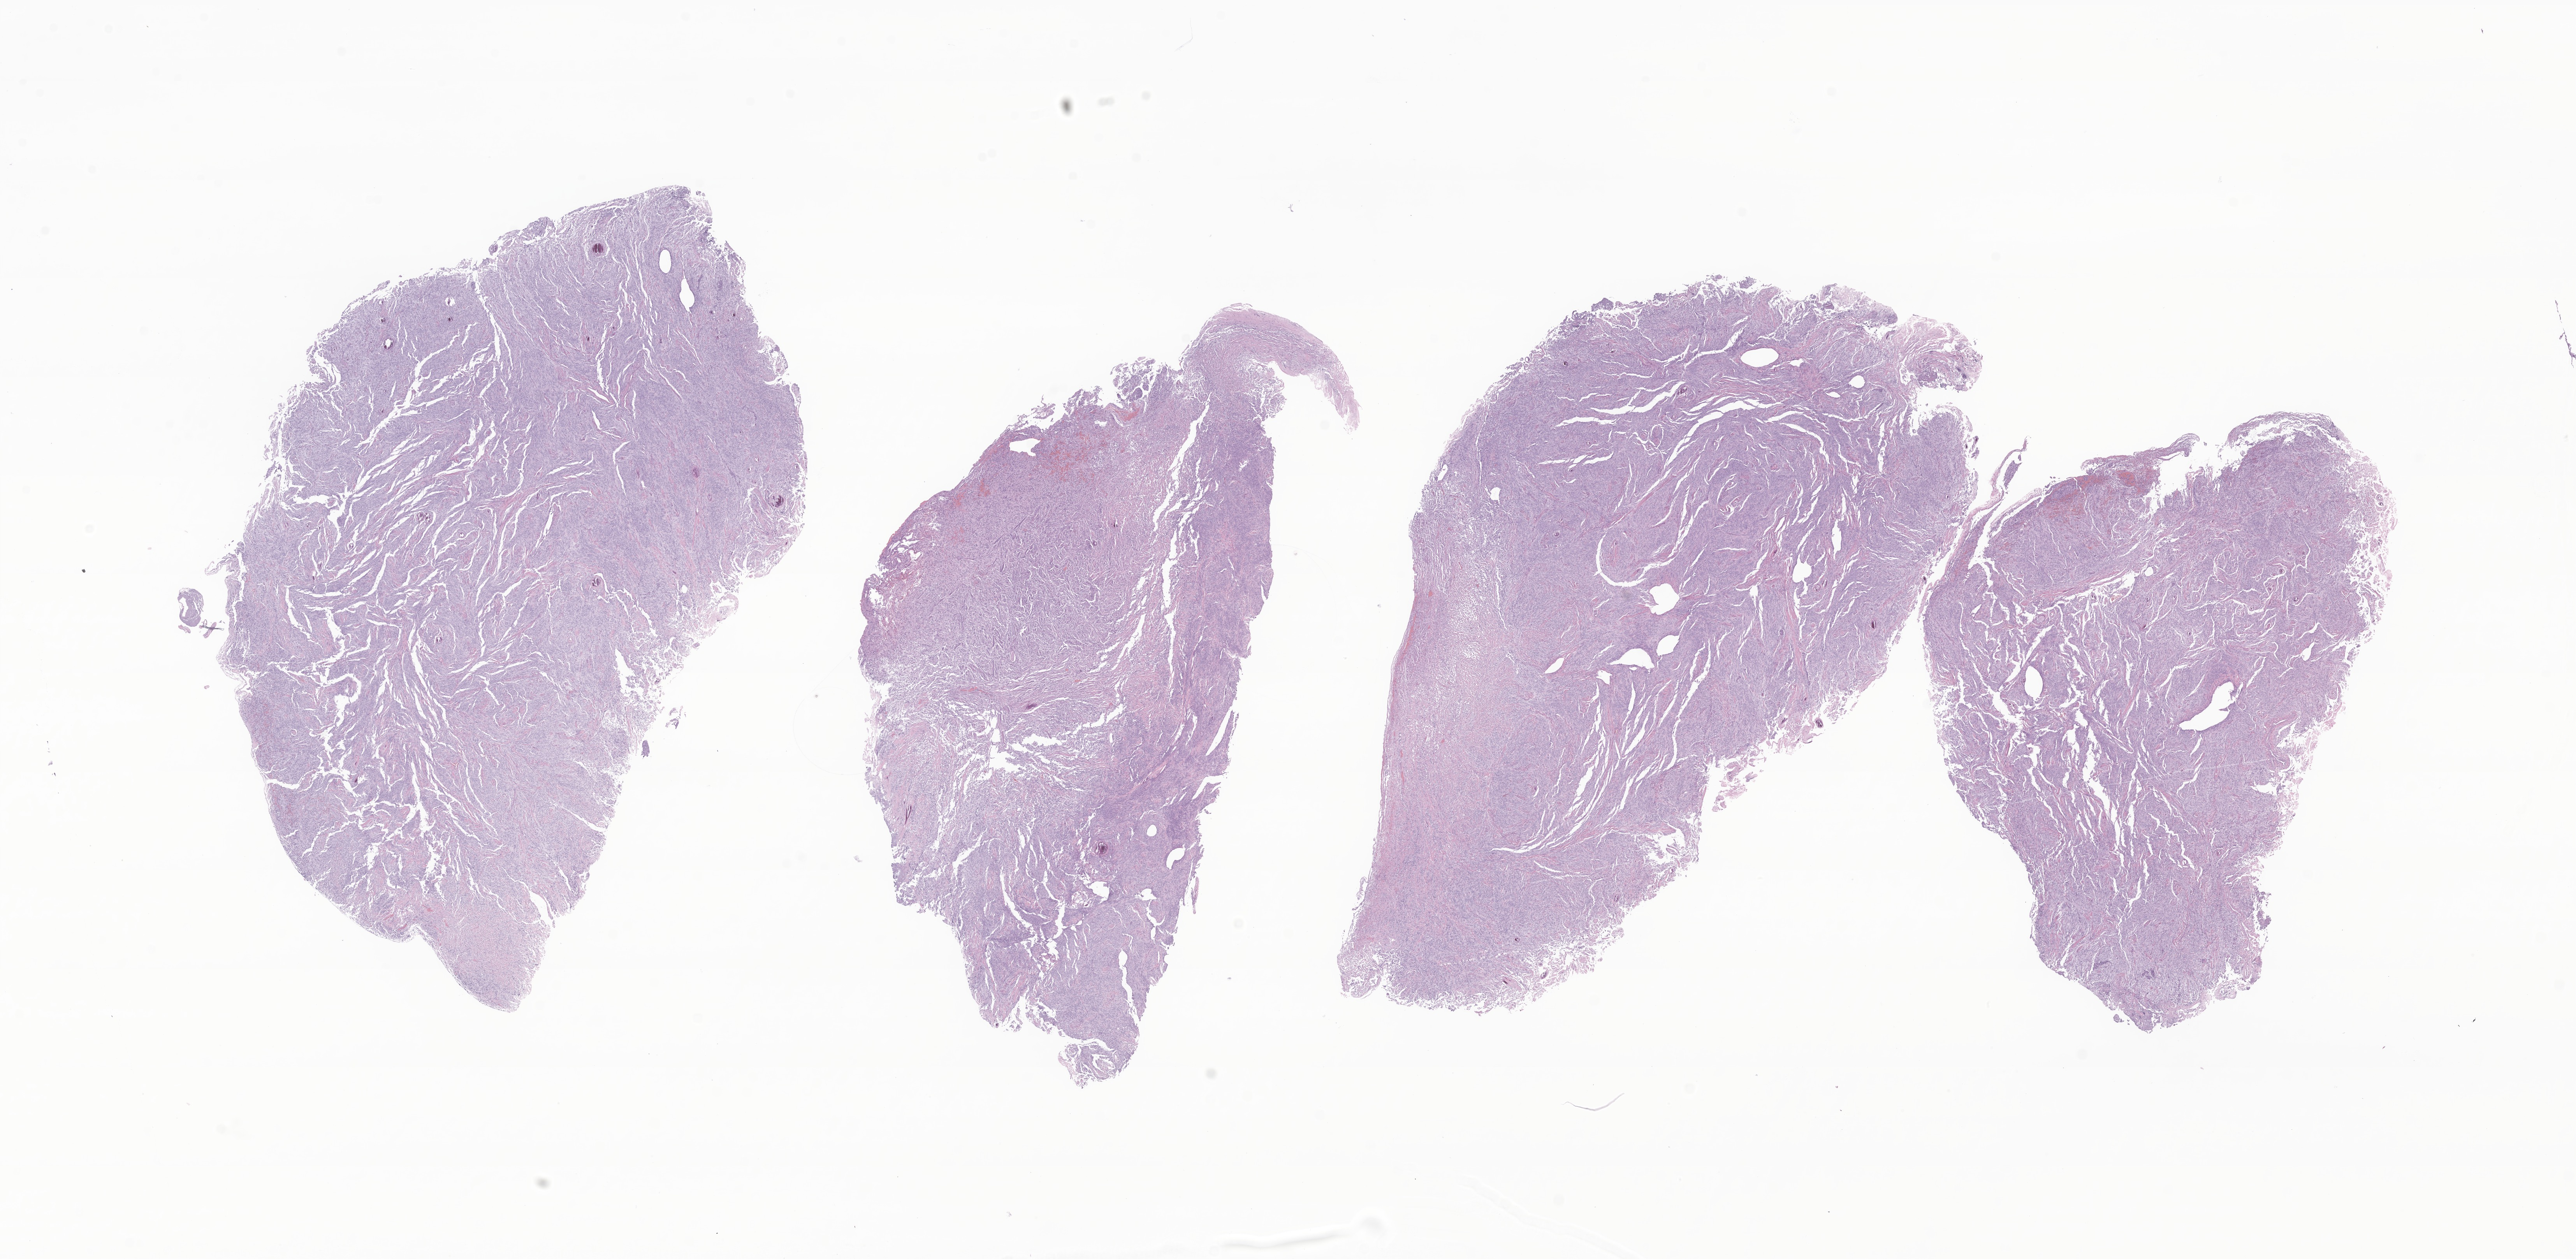
H&E whole-slide image of tumor tissue from the brain — low-resolution overview of the scanned area, about 27.9 x 13.6 mm, FFPE section. Male patient, age 141 months (11 years 9 months).
• recorded diagnosis: Meningioma, NOS